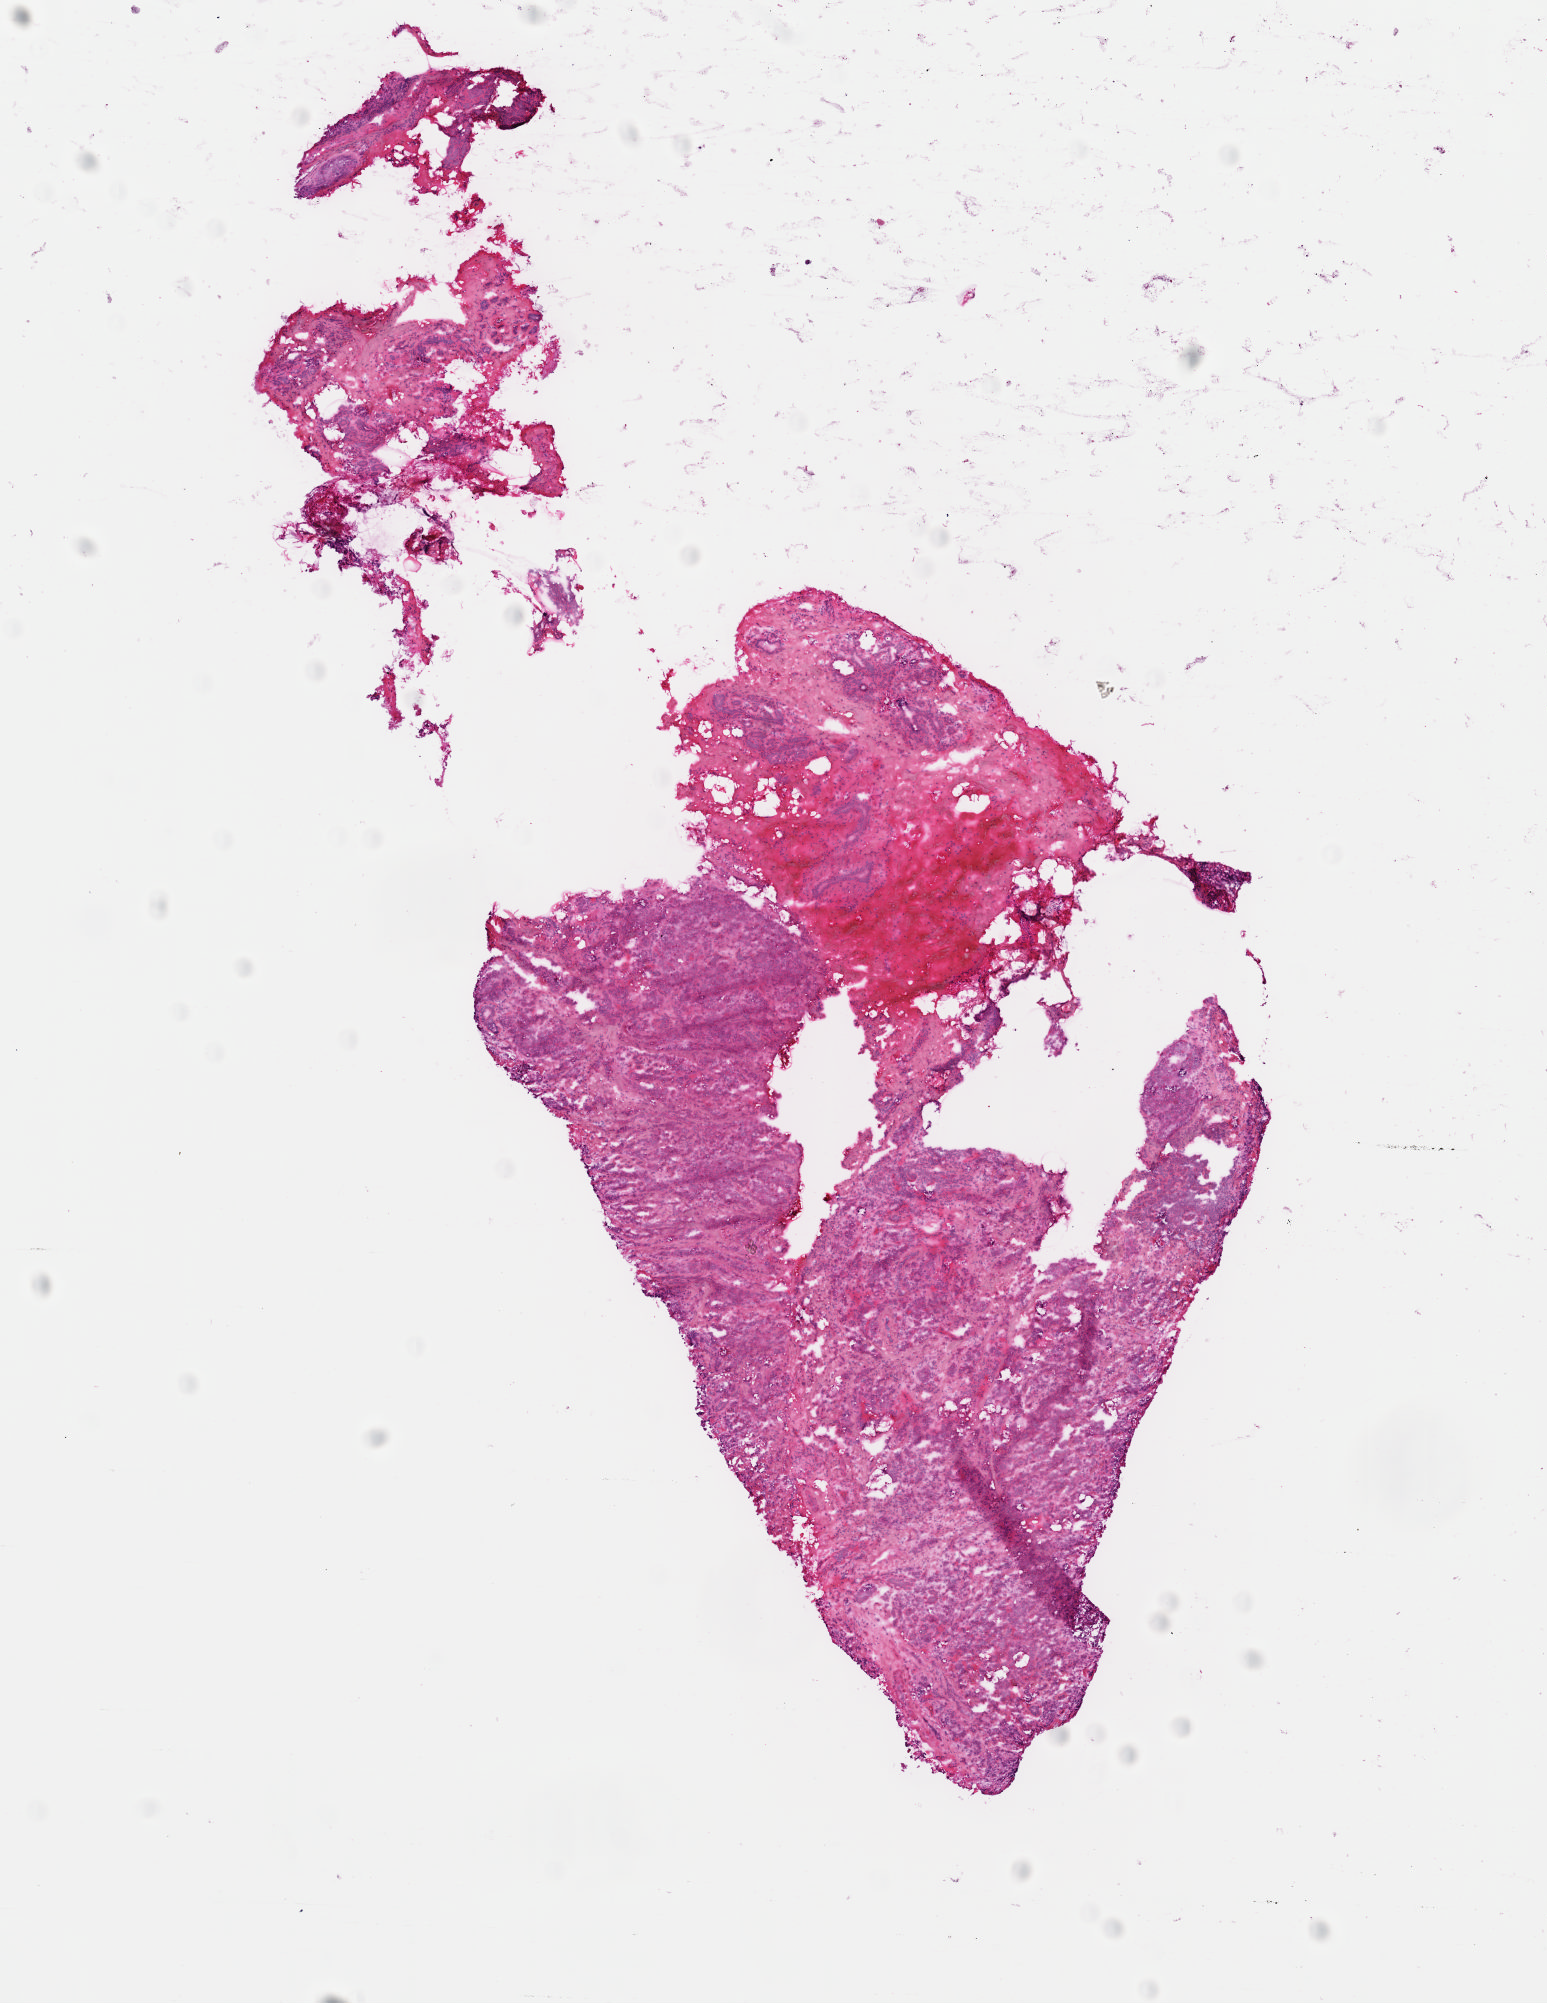
H&E whole-slide image — low-resolution overview of the scanned area, about 6.1 x 7.9 mm (acquisition: 40x scan), frozen section, sample: primary tumour, breast. Female patient; age at initial diagnosis 44 years. Pathologist review of this section (percent, as recorded): tumour cells 75%, tumour nuclei 75%, normal cells 0%, stromal cells 25%, necrosis 0%. Inflammatory infiltration, as recorded: lymphocyte infiltration 3%, monocyte infiltration 1%, neutrophil infiltration 1%.
AJCC pathologic stage: IIIA (6th edition). Diagnosis: Infiltrating duct carcinoma, NOS. Lymph nodes positive (case pathology): 6 of 22 examined.